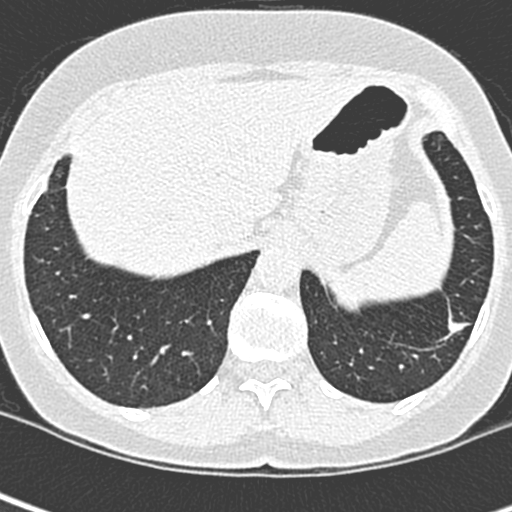
Low-dose screening chest CT, one axial slice; slice 54 of 252 in the series (ordered by position); 120 kVp; lung window (W 1500 / L -600 HU); 1.3 mm slice thickness; 512 × 512 image matrix, field of view 271 × 271 mm.
Outlined on this slice (expert manual segmentation):
- lesion 1 (tumor, lower lobe of left lung): bounding box [x1, y1, x2, y2] px = [448, 316, 466, 335]